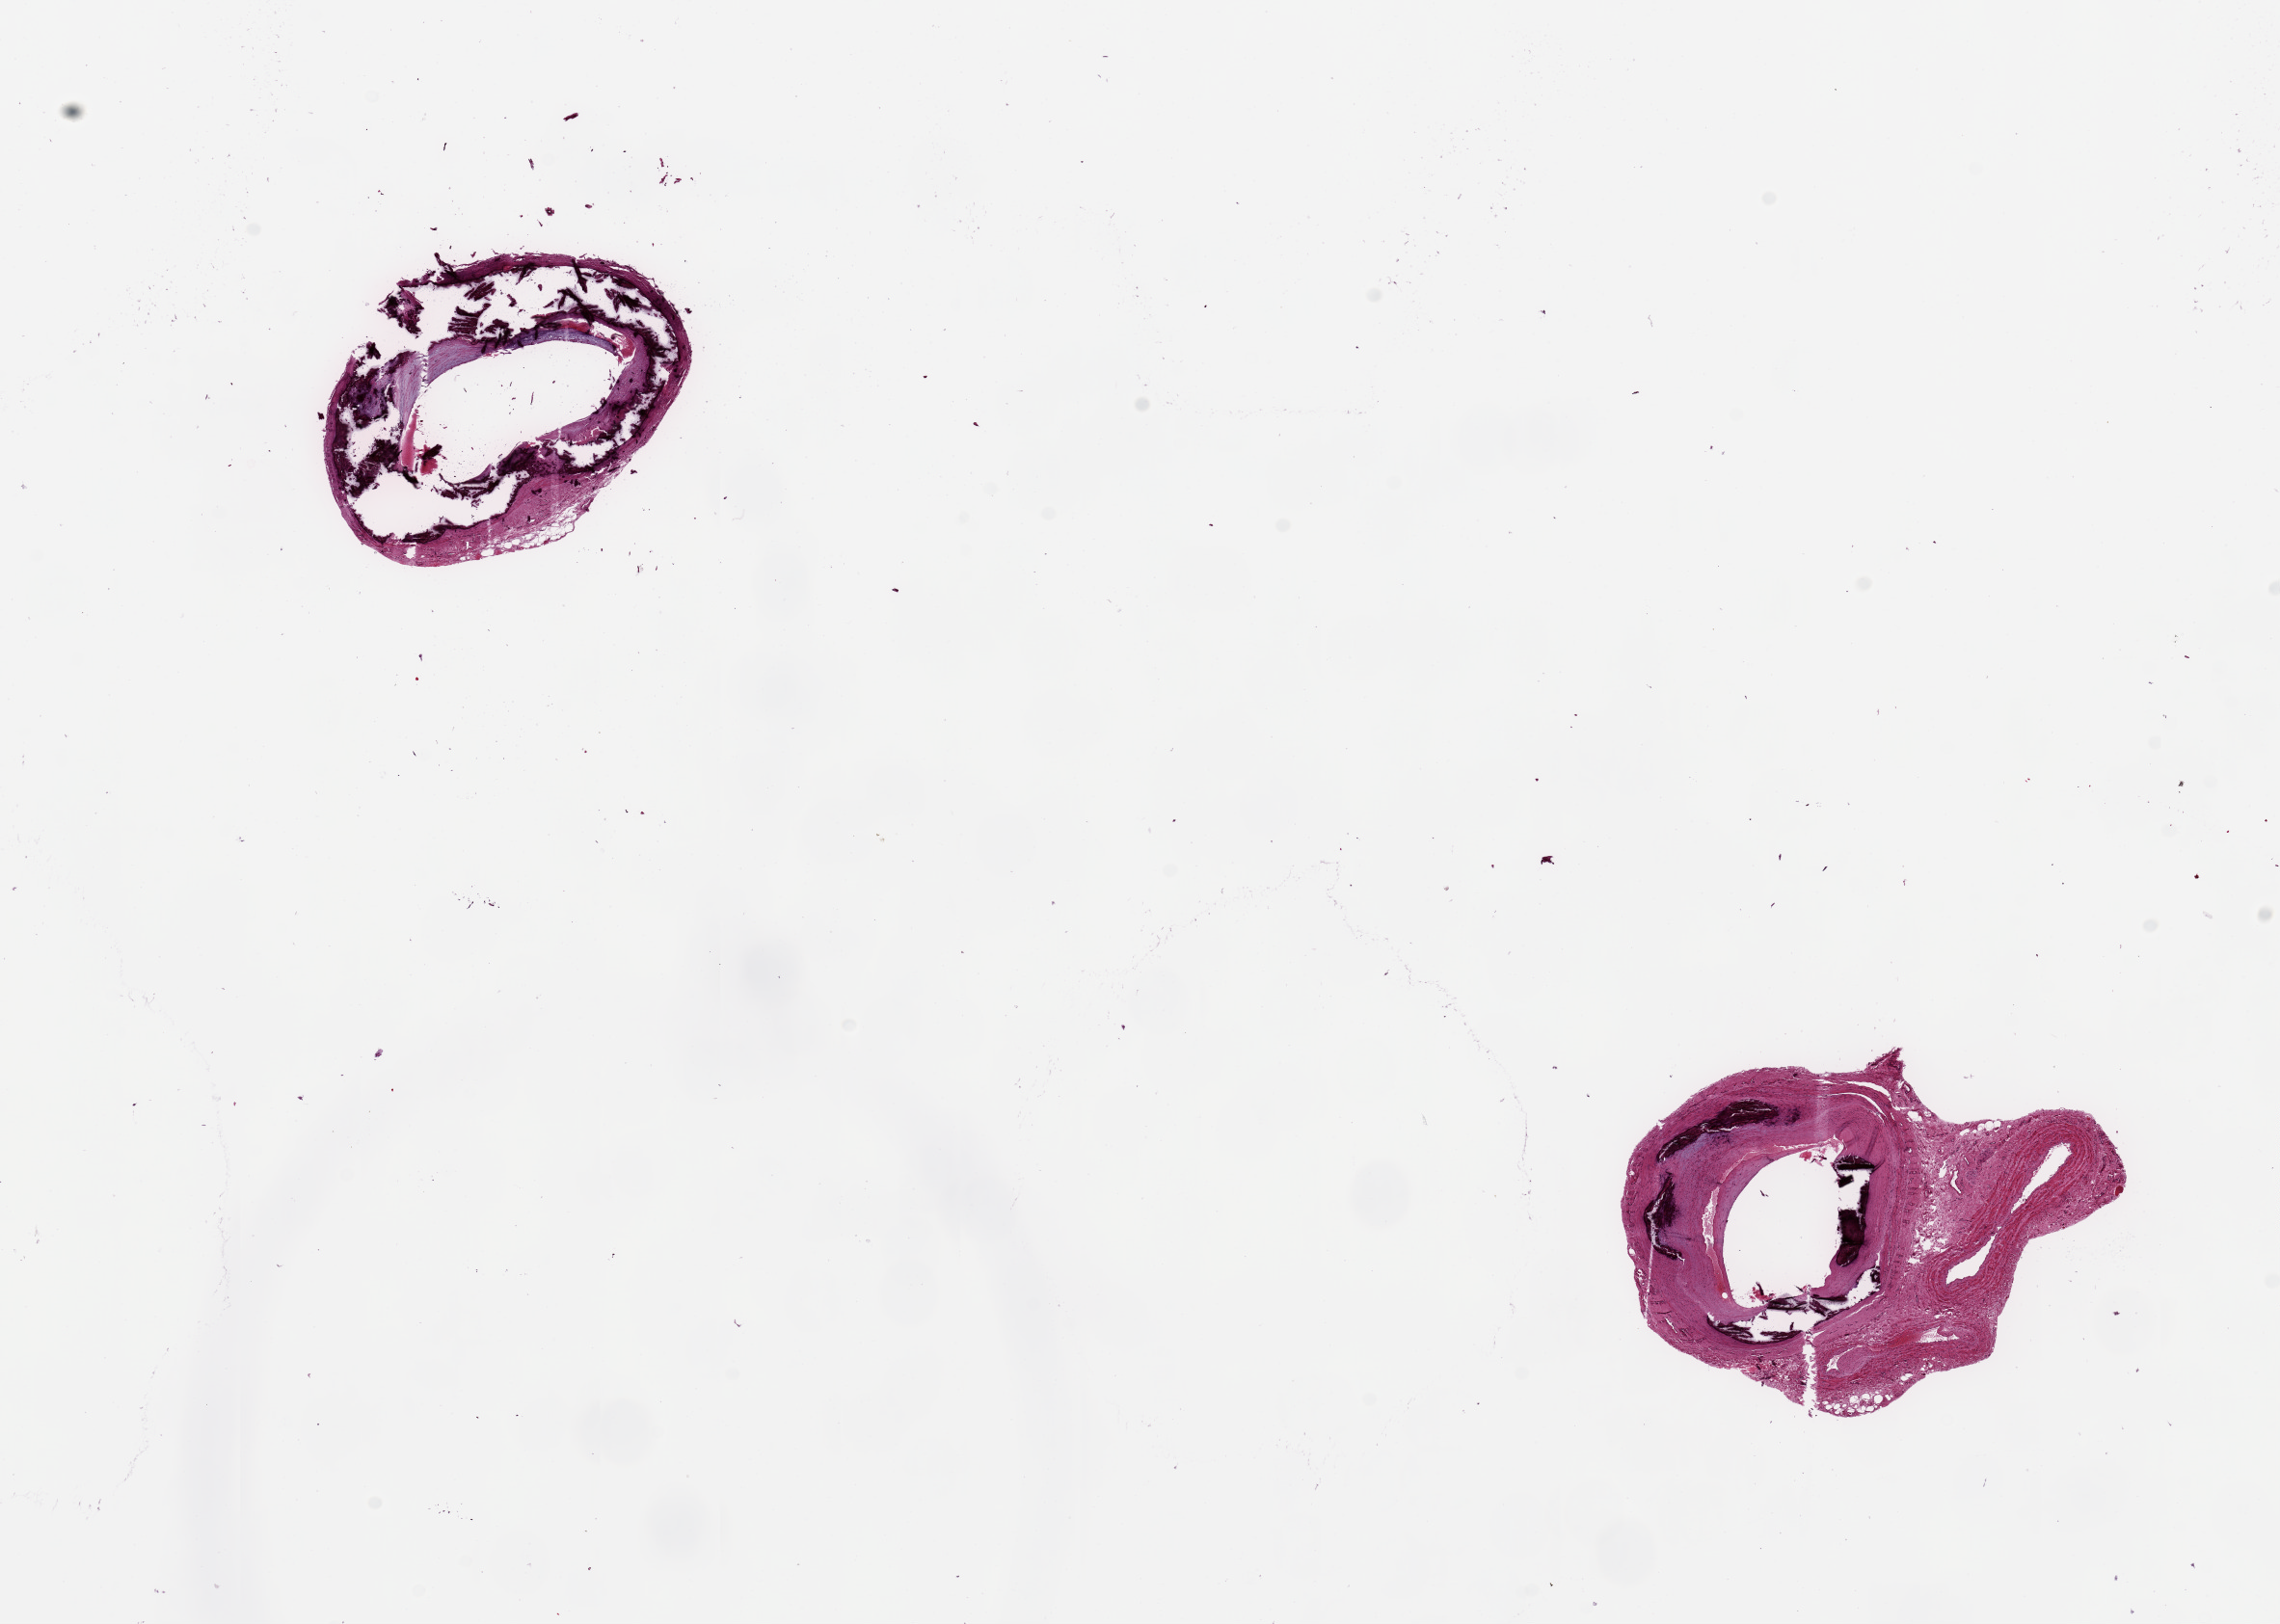
Whole-slide image, haematoxylin and eosin stain — a low-resolution overview of the entire scanned area, about 18.7 x 13.3 mm; PAXgene-fixed, paraffin-embedded tissue; target tissue: tibial artery; tissue donor sample. Donor sex: male.
Pathologist's review note for this sample: 2 ~3mm pieces. Mild atheromatous luminal deposits, severe Monckeberg???s medial sclerosis.